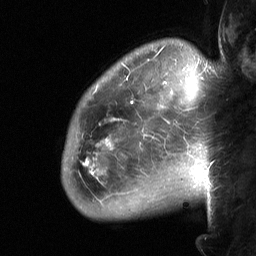
Breast MRI (dynamic contrast-enhanced), one sagittal slice. Position 53 of 64 along the scan axis. Dynamic contrast-enhanced study with each time point stored as its own series, time point 2 of 3 at this slice position (early post-contrast, ordered by acquisition time). 1.5 T. TE 4.8 ms, TR 27 ms. 2 mm slice thickness. 256 × 256 image matrix. Female patient, age 50 years. Case-level facts recorded for this patient, not image findings: setting: breast cancer imaged before/during neoadjuvant chemotherapy; receptor status: HER2-positive.
Annotated regions visible in this slice (semi-automatic segmentation, software-assisted and operator-edited):
- analysis volume of interest (the breast-tissue region the enhancement analysis was run in; not a lesion): box from (x=62, y=62) to (x=222, y=222) px
- tumour enhancement mask (voxels above the 90 % enhancement threshold inside the analysis volume of interest): (x=83, y=100)–(x=134, y=175)